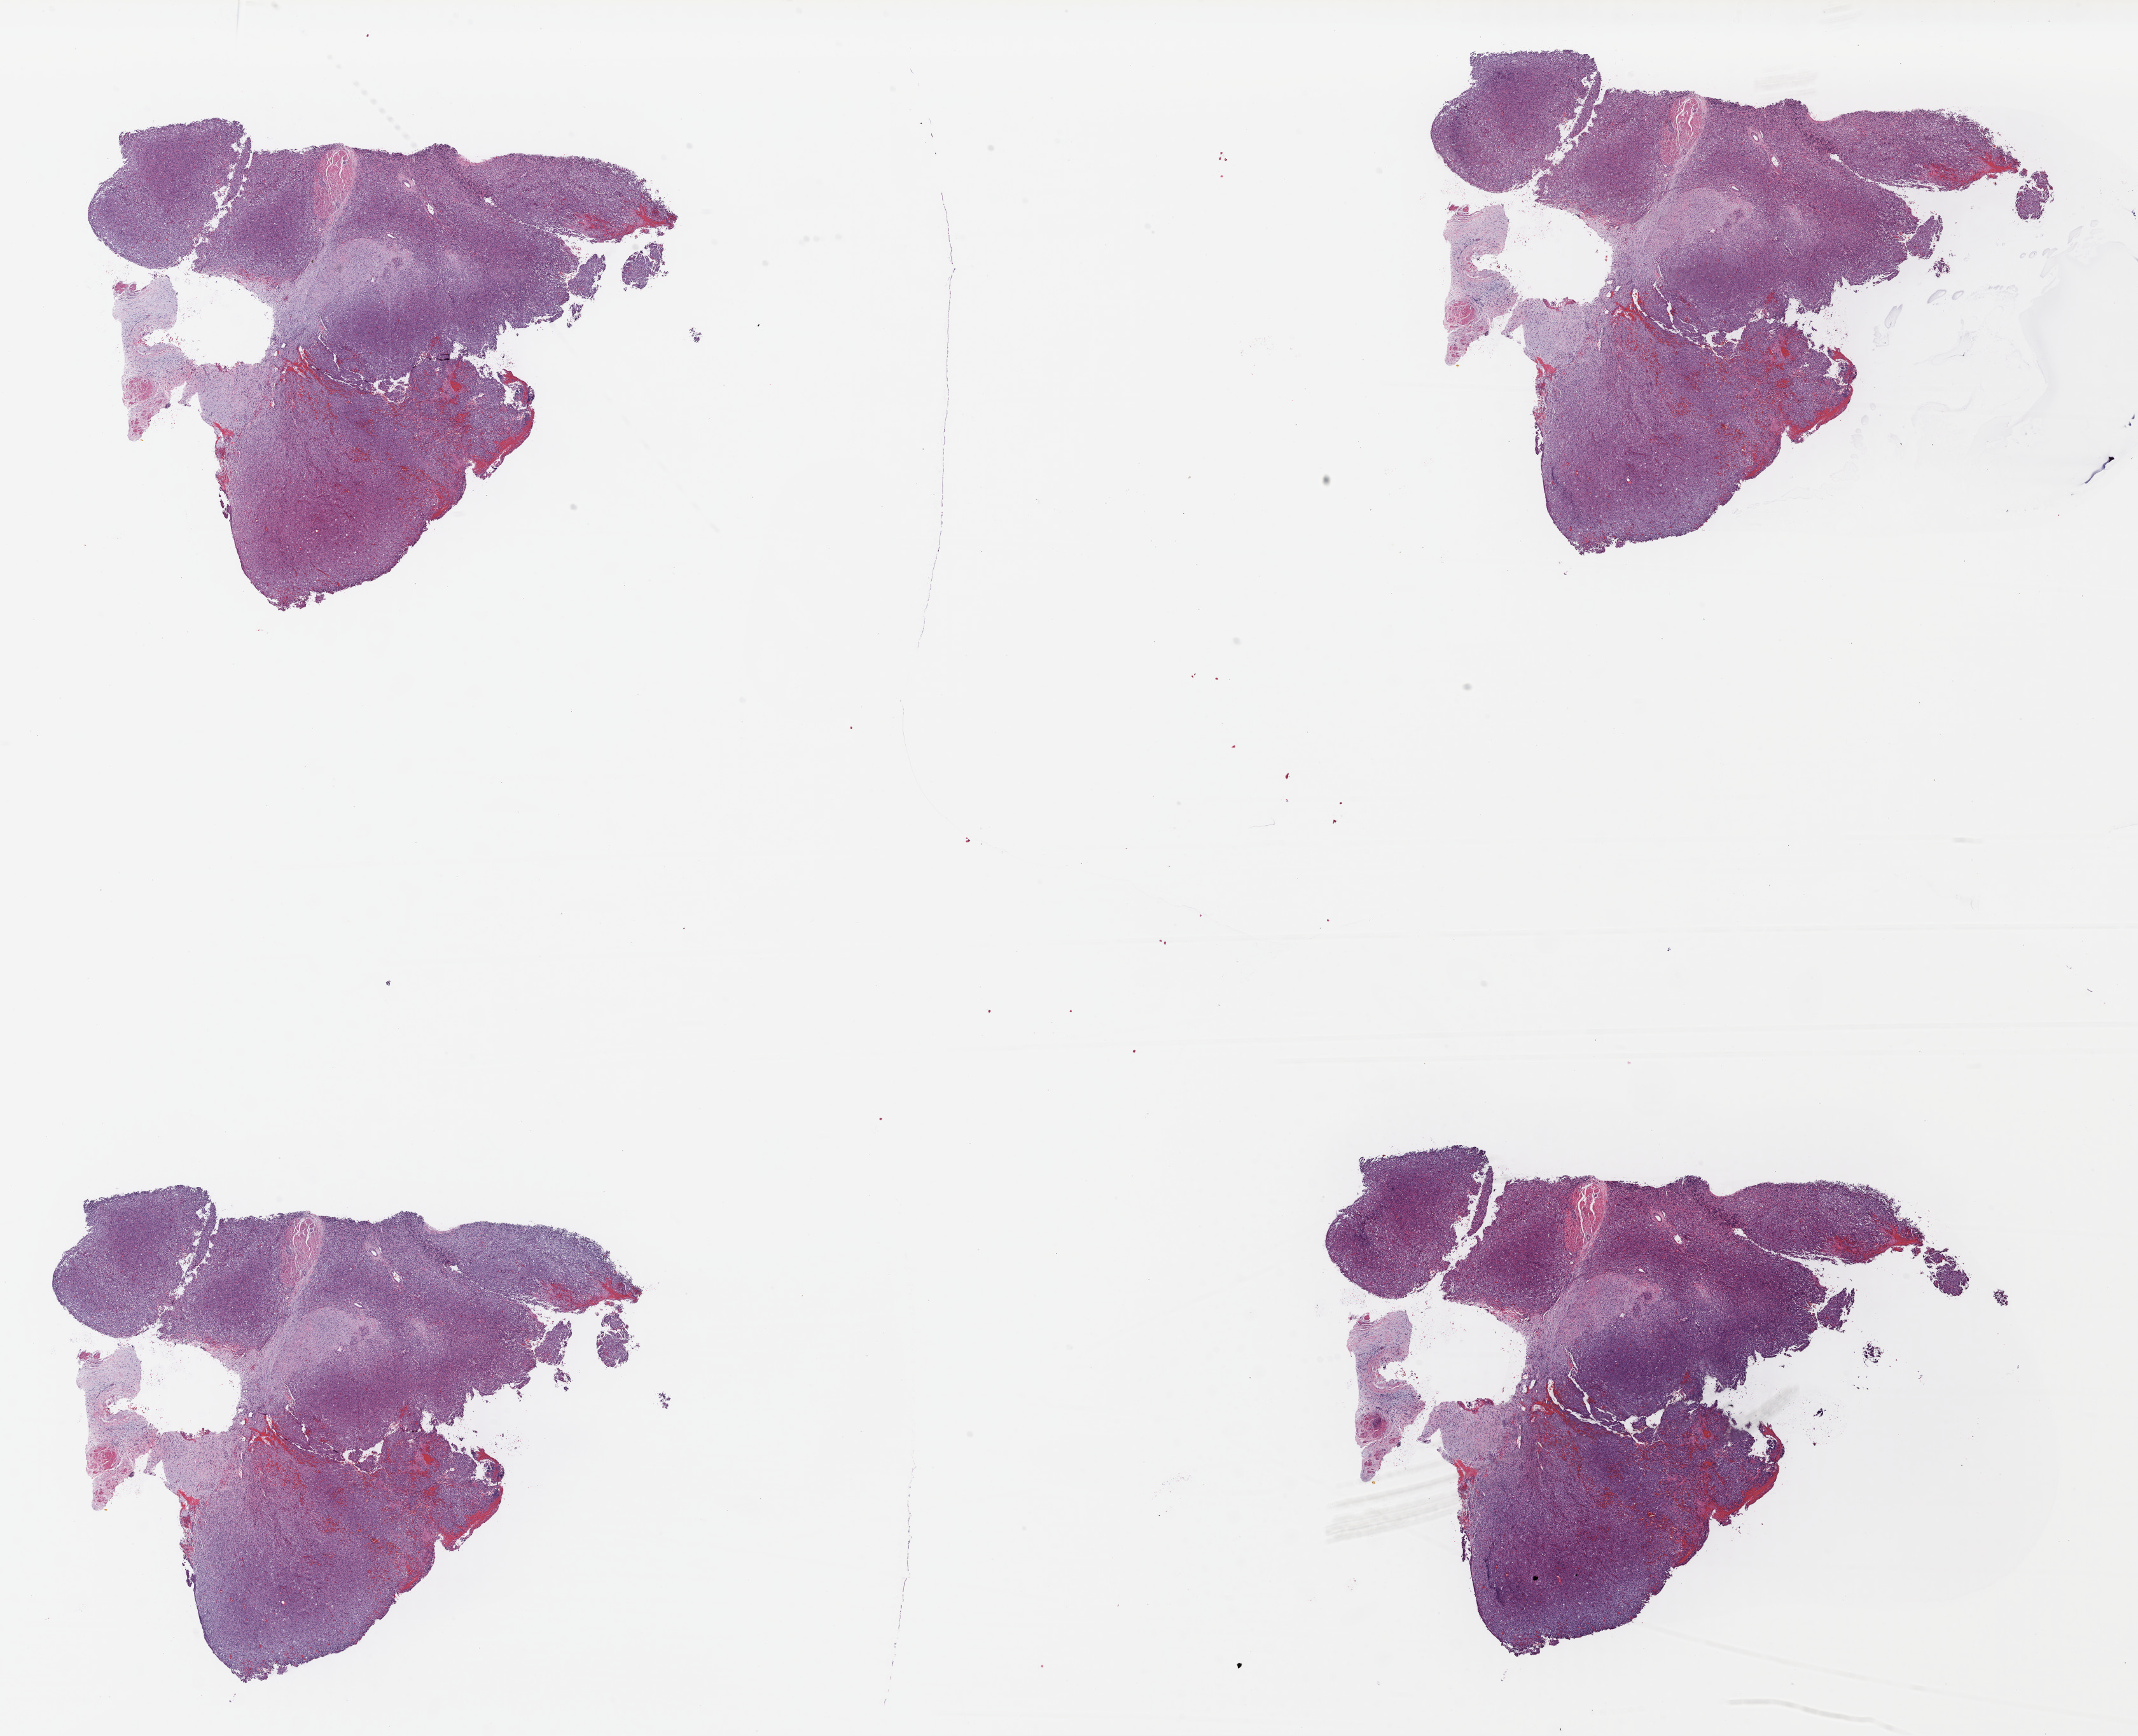
Hematoxylin and eosin (H&E) stained whole-slide image, whole scanned area (about 26.4 x 21.5 mm, slide scanned at 40x) shown as a low-resolution overview, formalin-fixed paraffin-embedded (FFPE) diagnostic section, bladder, primary tumour sample. Patient: female, age at initial diagnosis 57 years. Histologic grade: high grade.
* TNM: T3 N0 M0
* histologic diagnosis: Transitional cell carcinoma
* AJCC pathologic stage: III (7th edition)